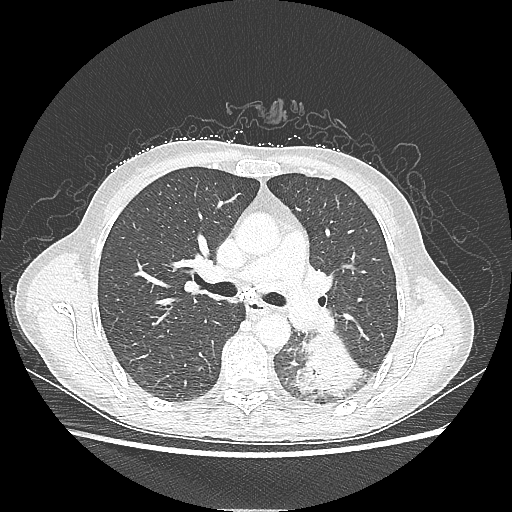
Chest CT, one axial slice; position 134 of 220 along the scan axis; reconstruction kernel LUNG; 80 kVp; lung window (W 1500 / L -600 HU); 1.25 mm slice thickness; 512 × 512 image matrix. Patient: female, 53 years. Case-level facts recorded for this patient, not image findings: clinical TNM (as recorded): T3 N0 M0.
Structures marked on this image (bounding box drawn by a radiologist):
- lung tumour (recorded histology: adenocarcinoma): bounding box [x1, y1, x2, y2] px = [294, 334, 365, 400]